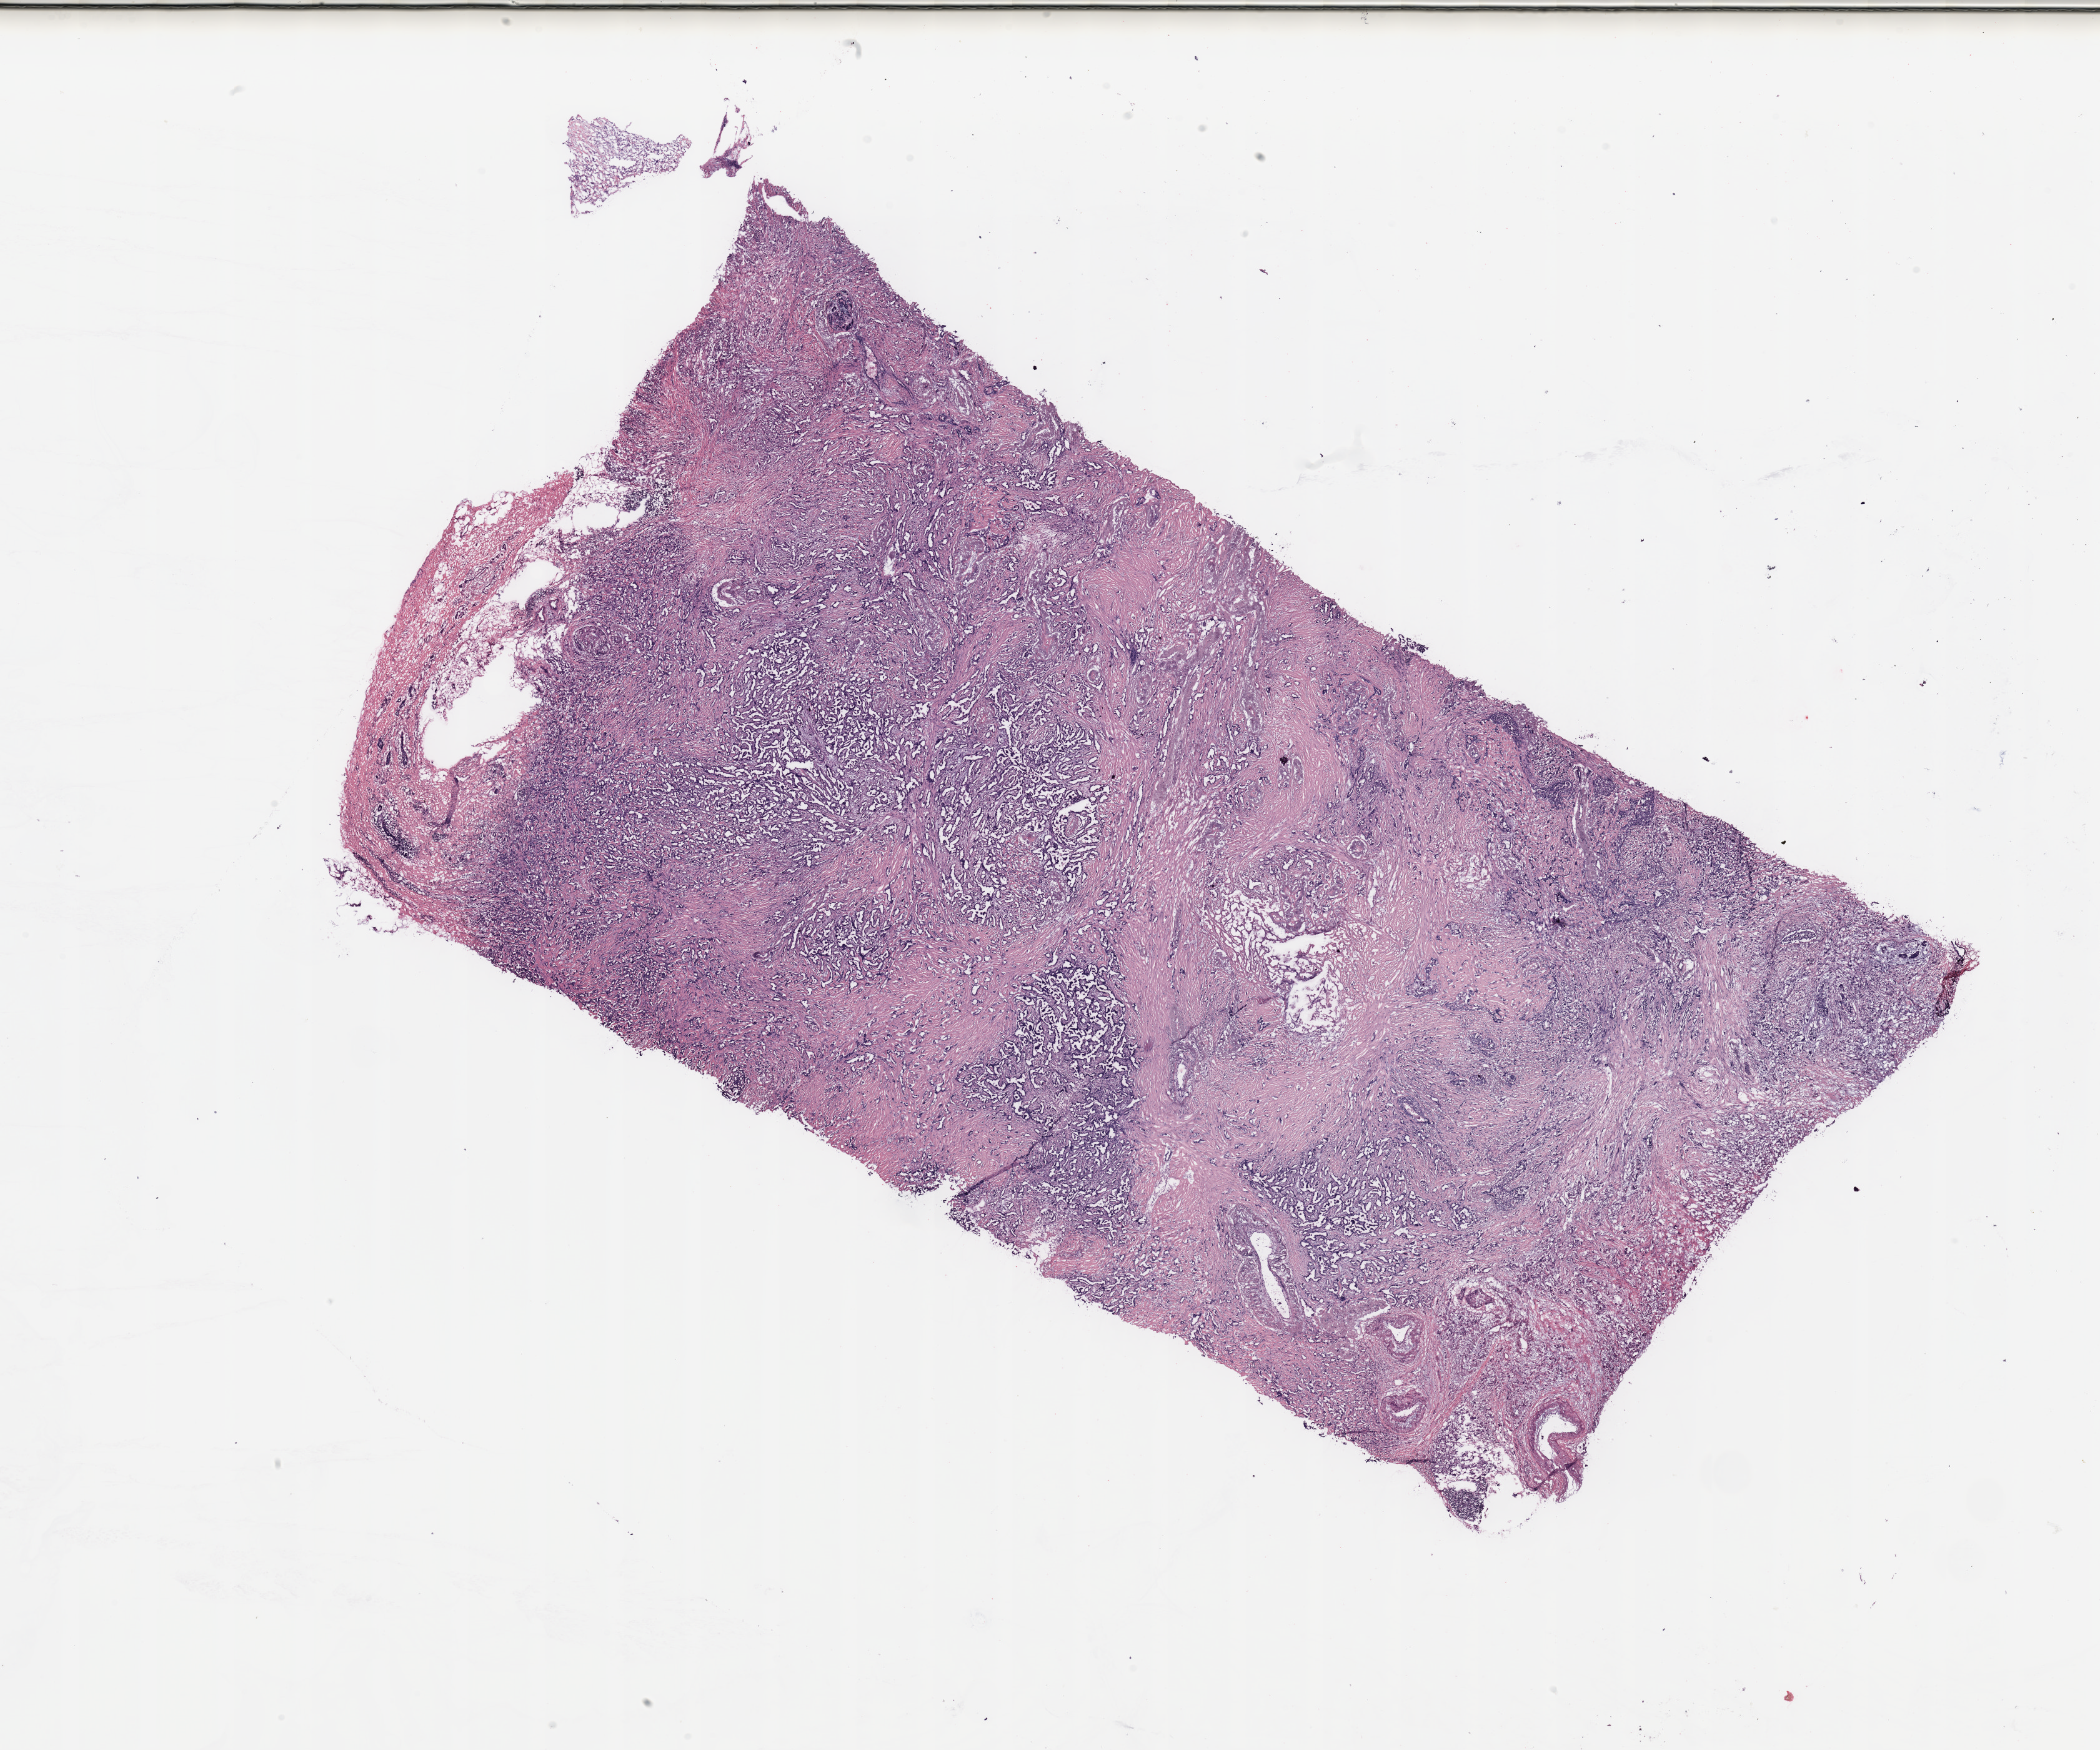
Hematoxylin and eosin (H&E) stained whole-slide image — low-resolution overview of the scanned area, about 26.6 x 22.2 mm (from a 20x scan); breast, tumour tissue. 59-year-old female patient.
- AJCC pathologic stage: IIA
- histologic diagnosis: Infiltrating lobular carcinoma, NOS